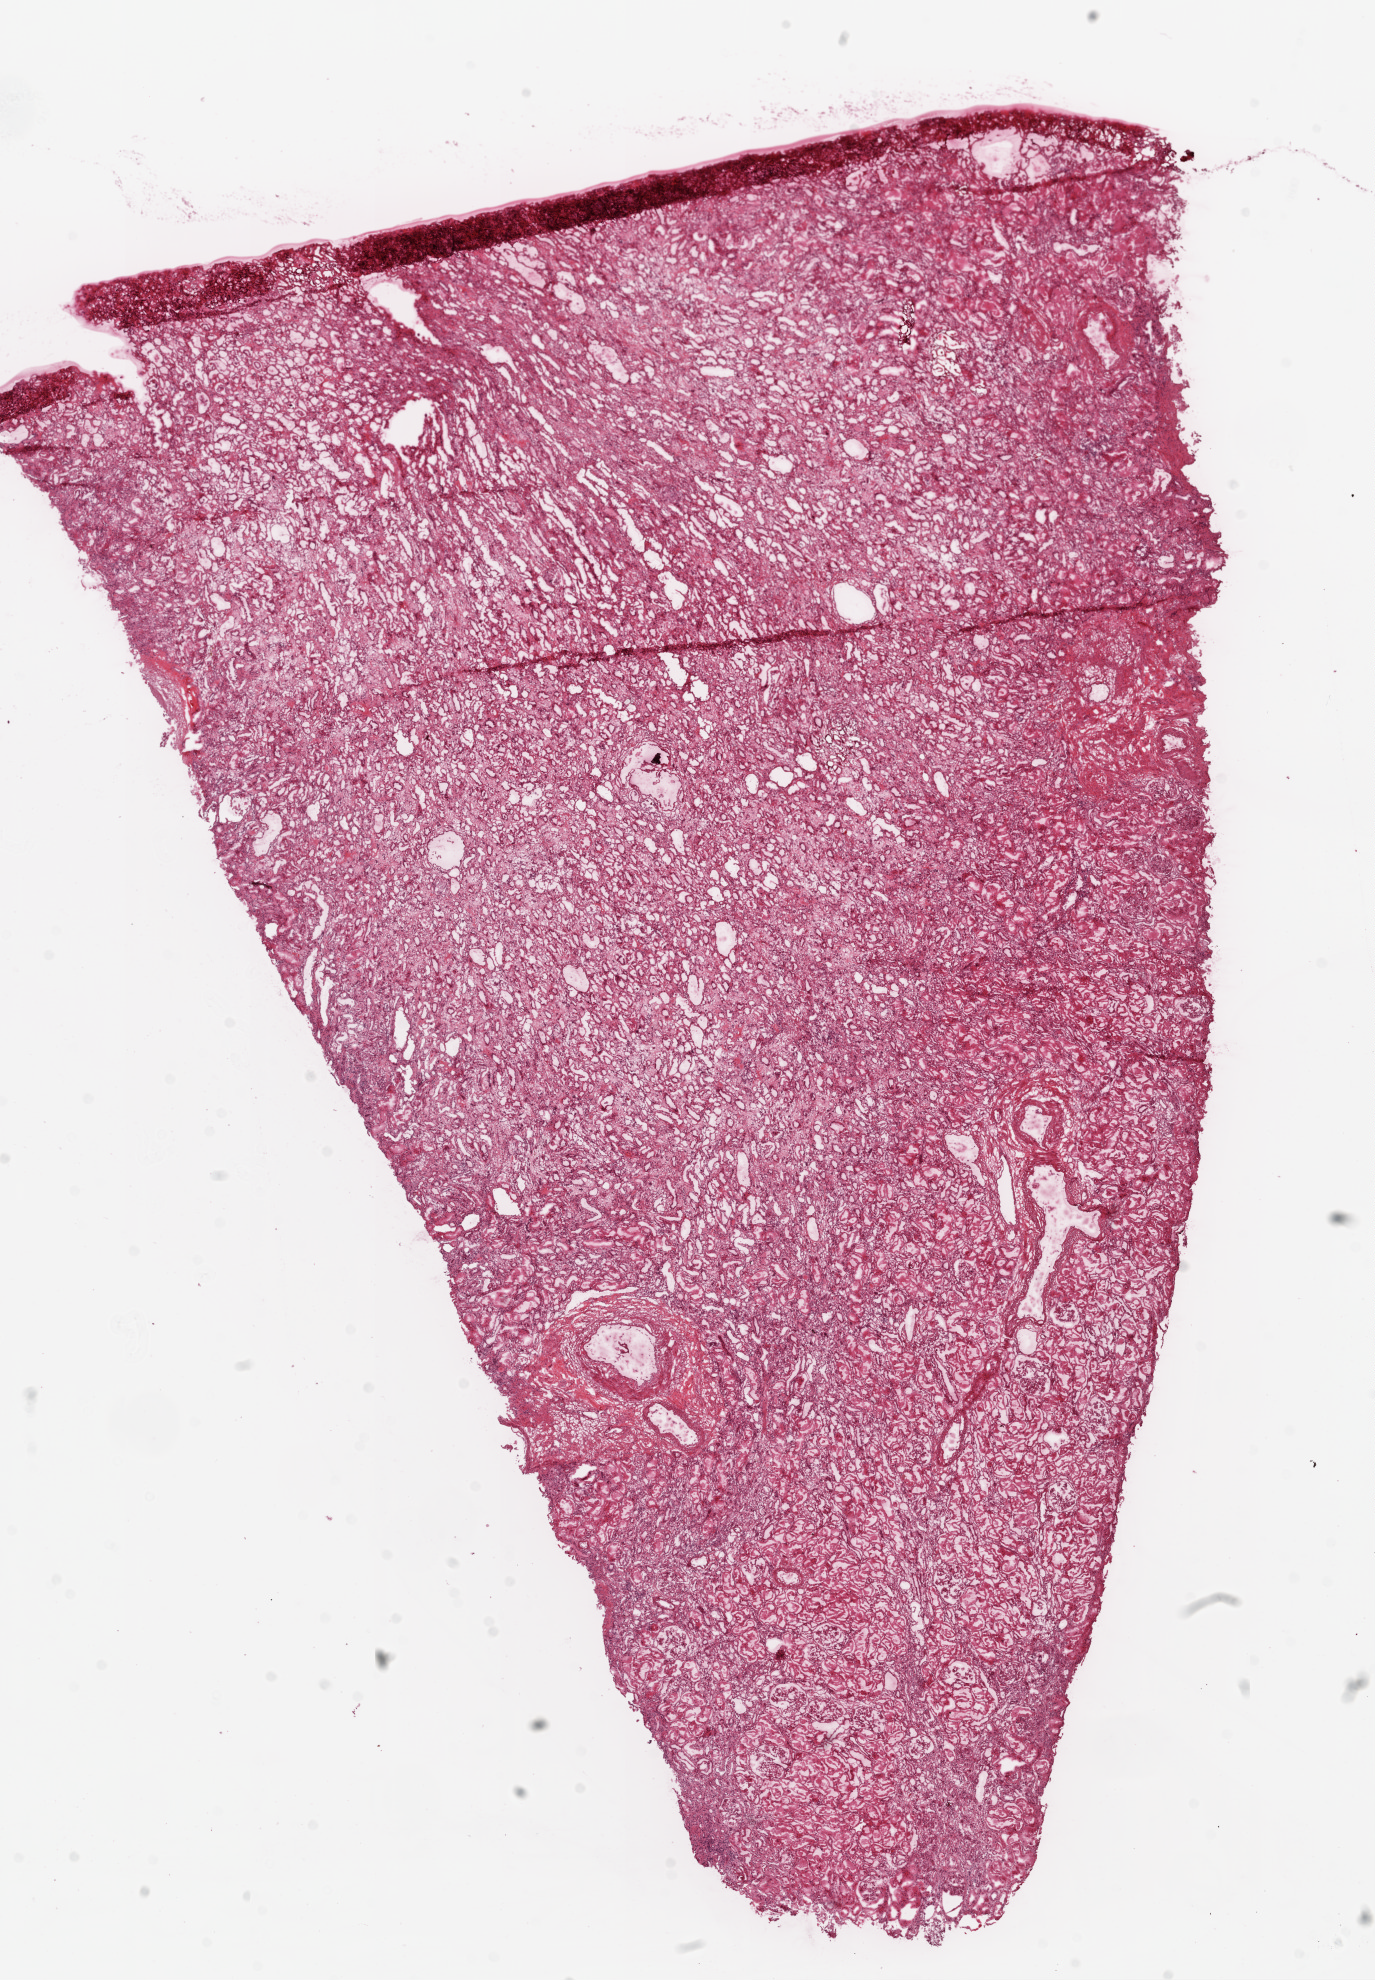
Digitized H&E tissue section (whole slide) — whole scanned area (about 11.0 x 15.9 mm, acquisition: 20x scan) shown as a low-resolution overview; frozen section from the top of the tissue portion; solid tissue normal (non-tumour tissue) sample from the kidney. Male, age 63 years at initial diagnosis.
- this section: solid tissue normal sample (biorepository sample class)
- patient diagnosis: Clear cell adenocarcinoma, NOS